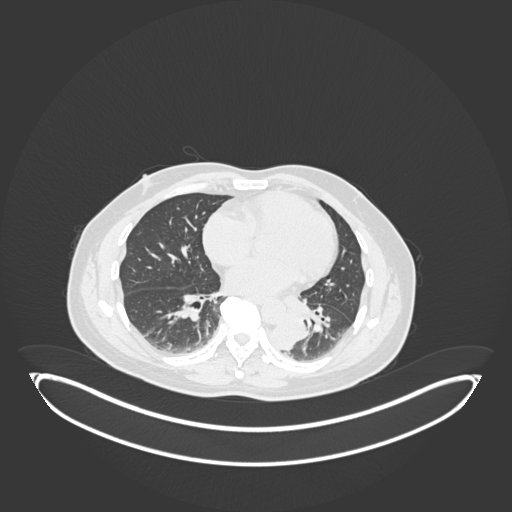
Chest CT, one axial slice. Slice 76 of 258 in the series (ordered by position). Reconstruction kernel B30f. Lung window (W 1500 / L -600 HU). 1 mm slice thickness. 512 × 512 image matrix. Patient: male, 54 years. Case-level facts recorded for this patient, not image findings: clinical TNM (as recorded): T3 N0 M0.
Structures marked on this image (rectangle marked by the reading radiologist):
- lung tumour (recorded histology: squamous cell carcinoma): bounding box (x1, y1, x2, y2) in pixels: (270, 298, 307, 353)